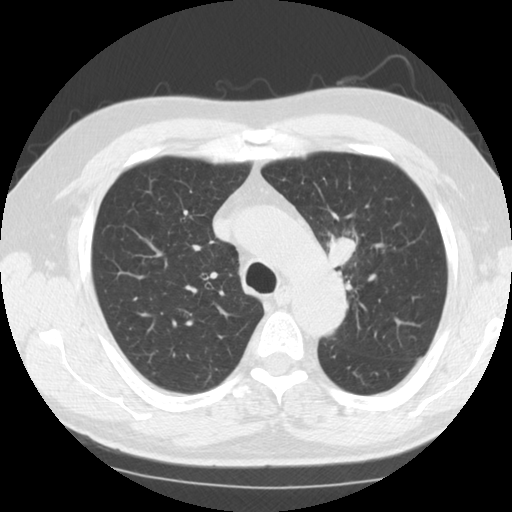
Axial slice from a low-dose chest CT screening exam; third annual screen; lung window (W 1500 / L -600 HU); 2.5 mm slice thickness; 512 × 512 image matrix. Male, age 60 years at enrolment. Current smoker at enrolment.
Lesion marked by an expert reader, bounding box [x1, y1, x2, y2] px = [318, 227, 371, 287]. Screening reader's record for this exam (one nodule recorded; not confirmed to be the boxed lesion): non-calcified nodule or mass ≥4 mm, left upper lobe, 24 × 21 mm, smooth margins, soft tissue attenuation, pre-existing on the prior screen: no. Official screen result: positive, other. Lung cancer was diagnosed 14 days after this screen: small cell carcinoma, NOS, left upper lobe, stage IIA (AJCC 6th edition), 26 mm at pathology.